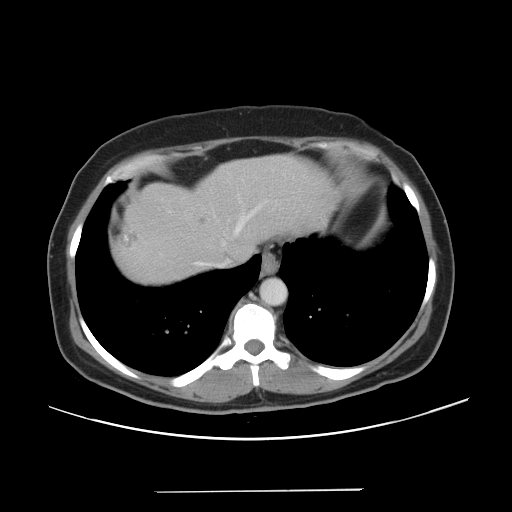
Contrast-enhanced abdominal CT, one axial slice; slice 41 of 56 in the series (ordered by position); 120 kVp; intravenous contrast given; soft-tissue window (W 400 / L 40 HU); 5 mm slice thickness; 512 × 512 image matrix, field of view 419 × 419 mm. Female patient, age 54 years. From the clinical record (not read from this slice): diagnosis: colorectal cancer liver metastases, imaged before liver resection; multiple liver metastases: yes; largest metastasis: 3.2 cm; disease in both lobes: yes.
Structures marked on this image (manually delineated by an expert):
- hepatic veins: bounding box (x1, y1, x2, y2) in pixels: (196, 205, 261, 265)
- liver: (116, 155, 334, 286)
- planned liver remnant (the part of the liver to remain after resection): (205, 155, 334, 259)
- liver metastasis: (119, 226, 136, 246)
- liver metastasis: (198, 217, 208, 227)